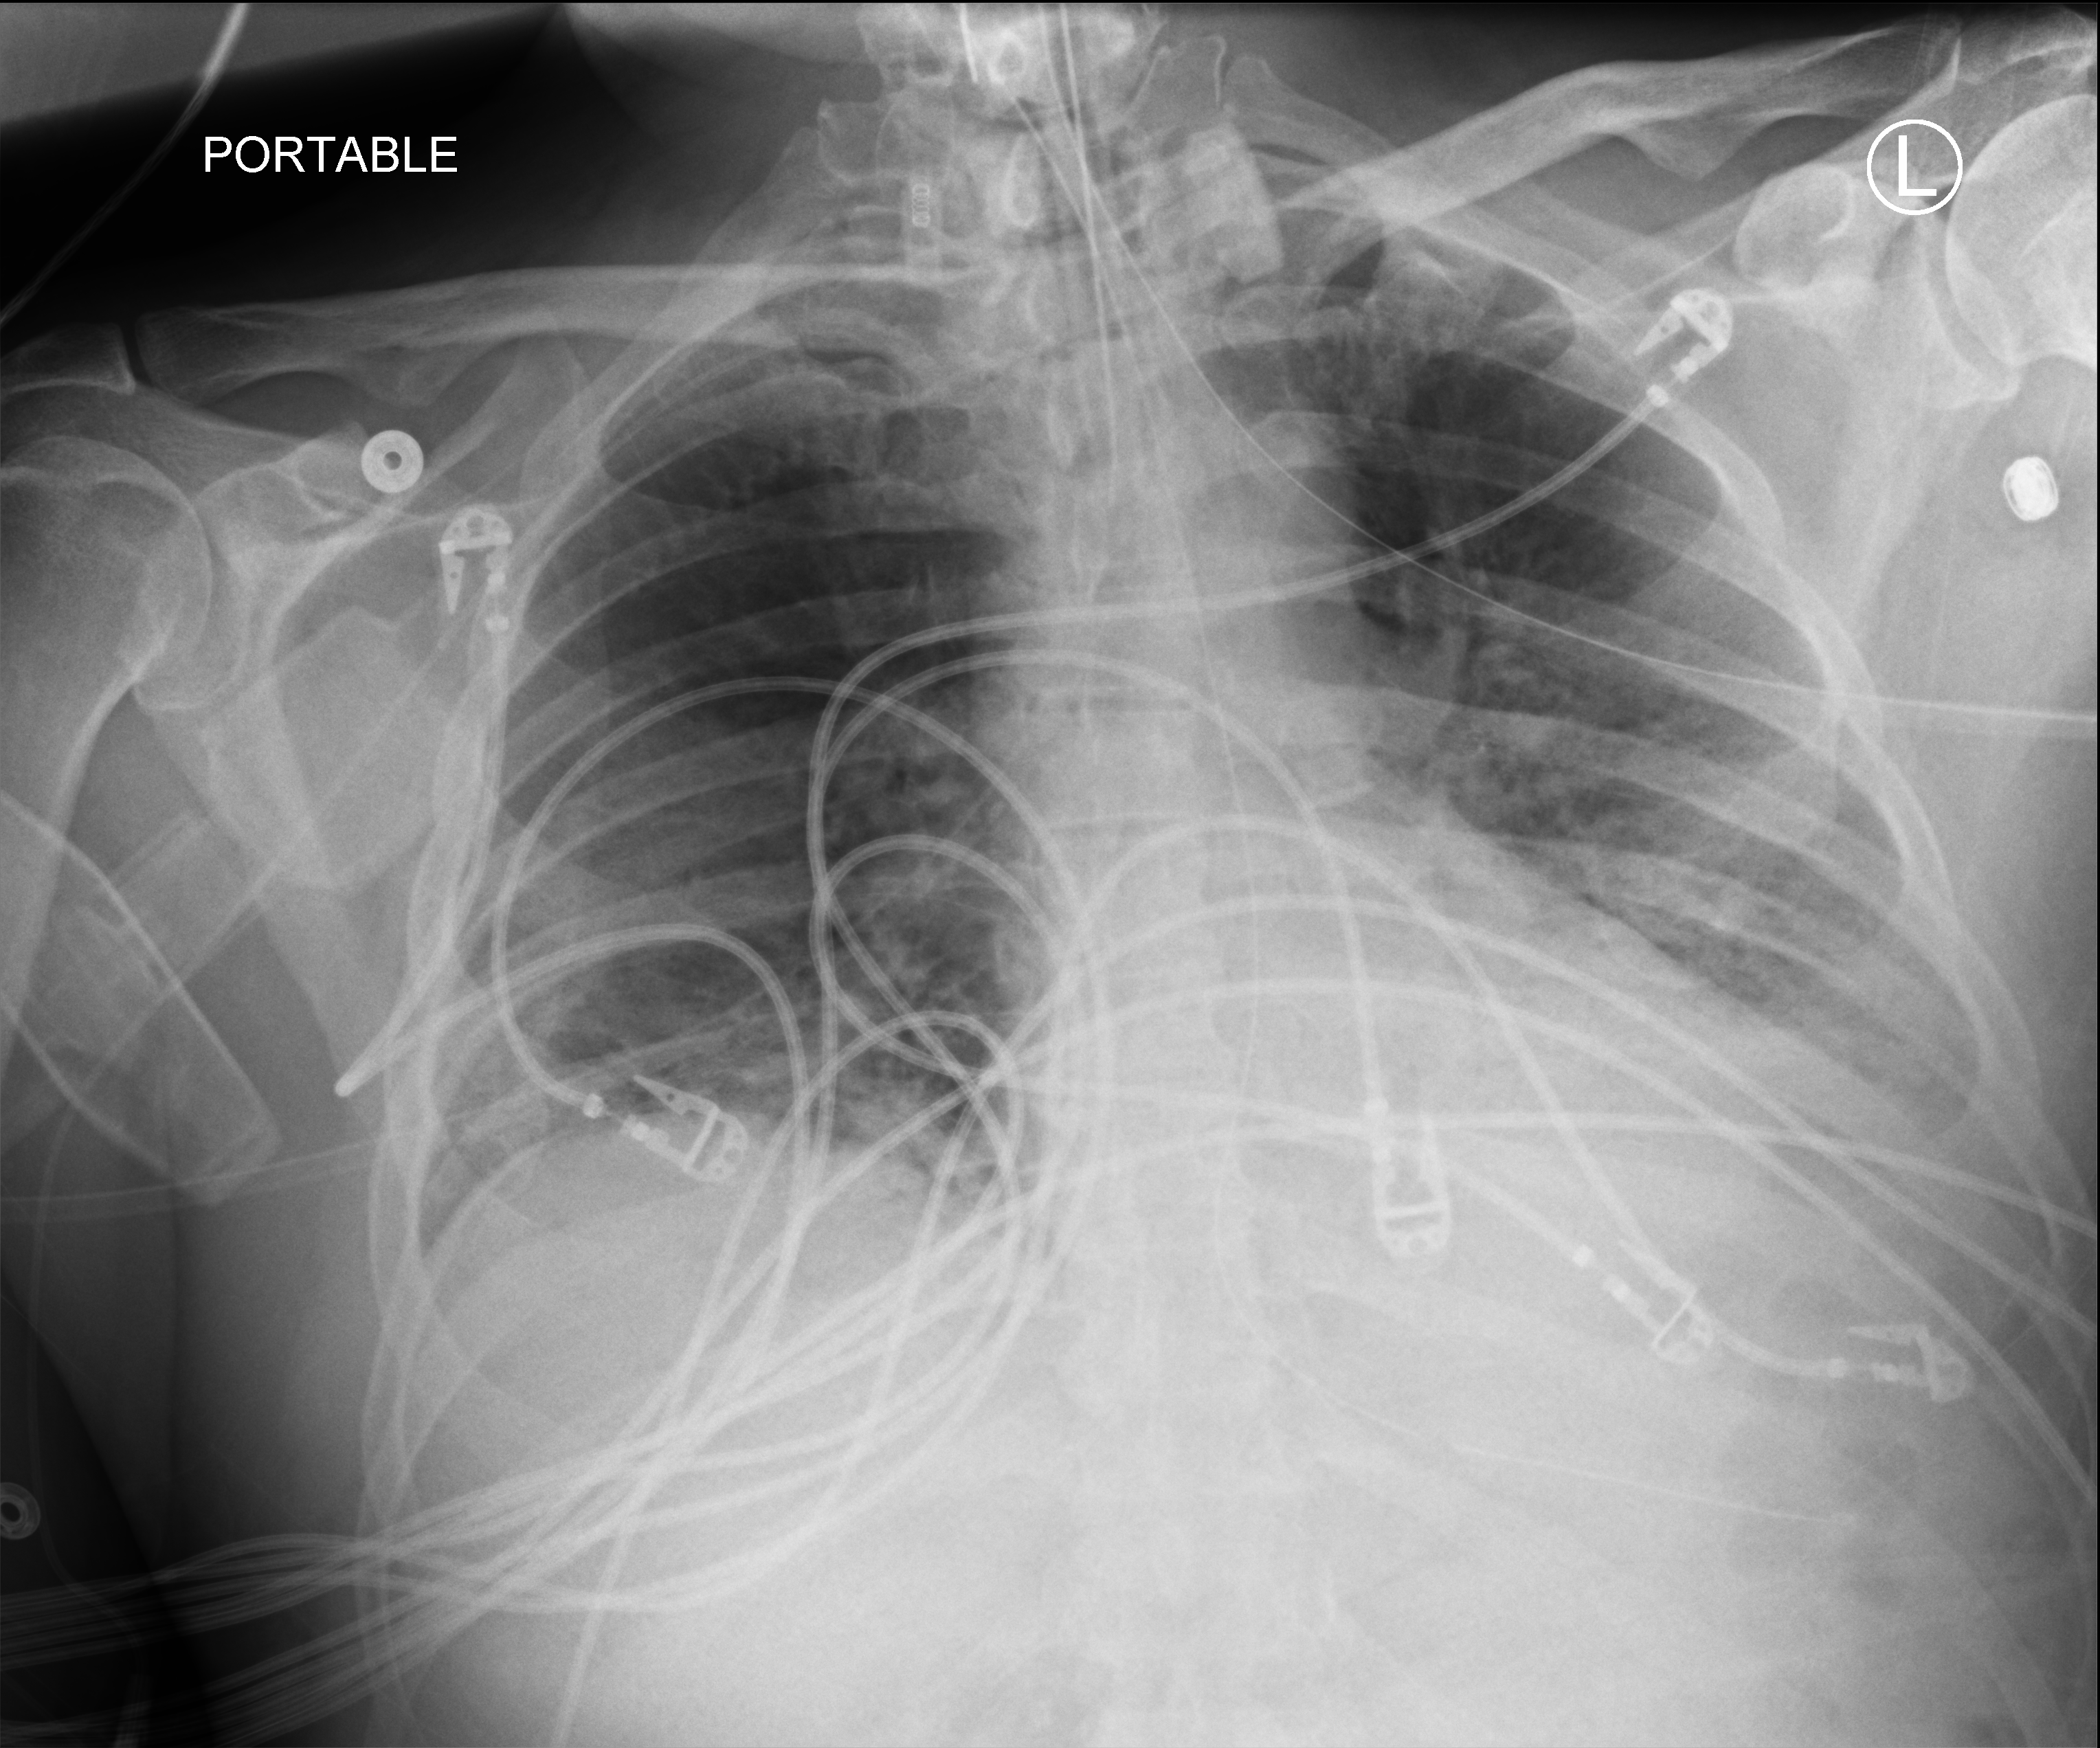
Portable chest radiograph. Patient hospitalised with COVID-19; male, aged 60–74 years.
Hospital-stay facts (about this admission, not read from this image; timing relative to this image not recorded): hypertension (admission record): no; admitted to intensive care during this hospital stay: yes; mechanically ventilated during this hospital stay: yes.